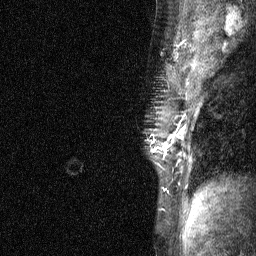
Breast MRI (dynamic contrast-enhanced), one sagittal slice; position 47 of 64 along the scan axis; dynamic contrast-enhanced study with each time point stored as its own series, time point 3 of 4 at this slice position (ordered by acquisition time); 1.5 T; TE 4.8 ms, TR 27 ms; 2 mm slice thickness; 256 × 256 image matrix, field of view 180 × 180 mm. Female patient, age 44 years. Case-level facts recorded for this patient, not image findings: setting: breast cancer imaged before/during neoadjuvant chemotherapy; receptor status: HR-positive, HER2-negative.
Annotated regions visible in this slice (semi-automatic segmentation, software-assisted and operator-edited):
- analysis volume of interest (the breast-tissue region the enhancement analysis was run in; not a lesion): bounding box <144,117,185,188> (left, top, right, bottom; pixels)
- tumour enhancement mask (voxels above the 90 % enhancement threshold inside the analysis volume of interest): <164,130,185,150>